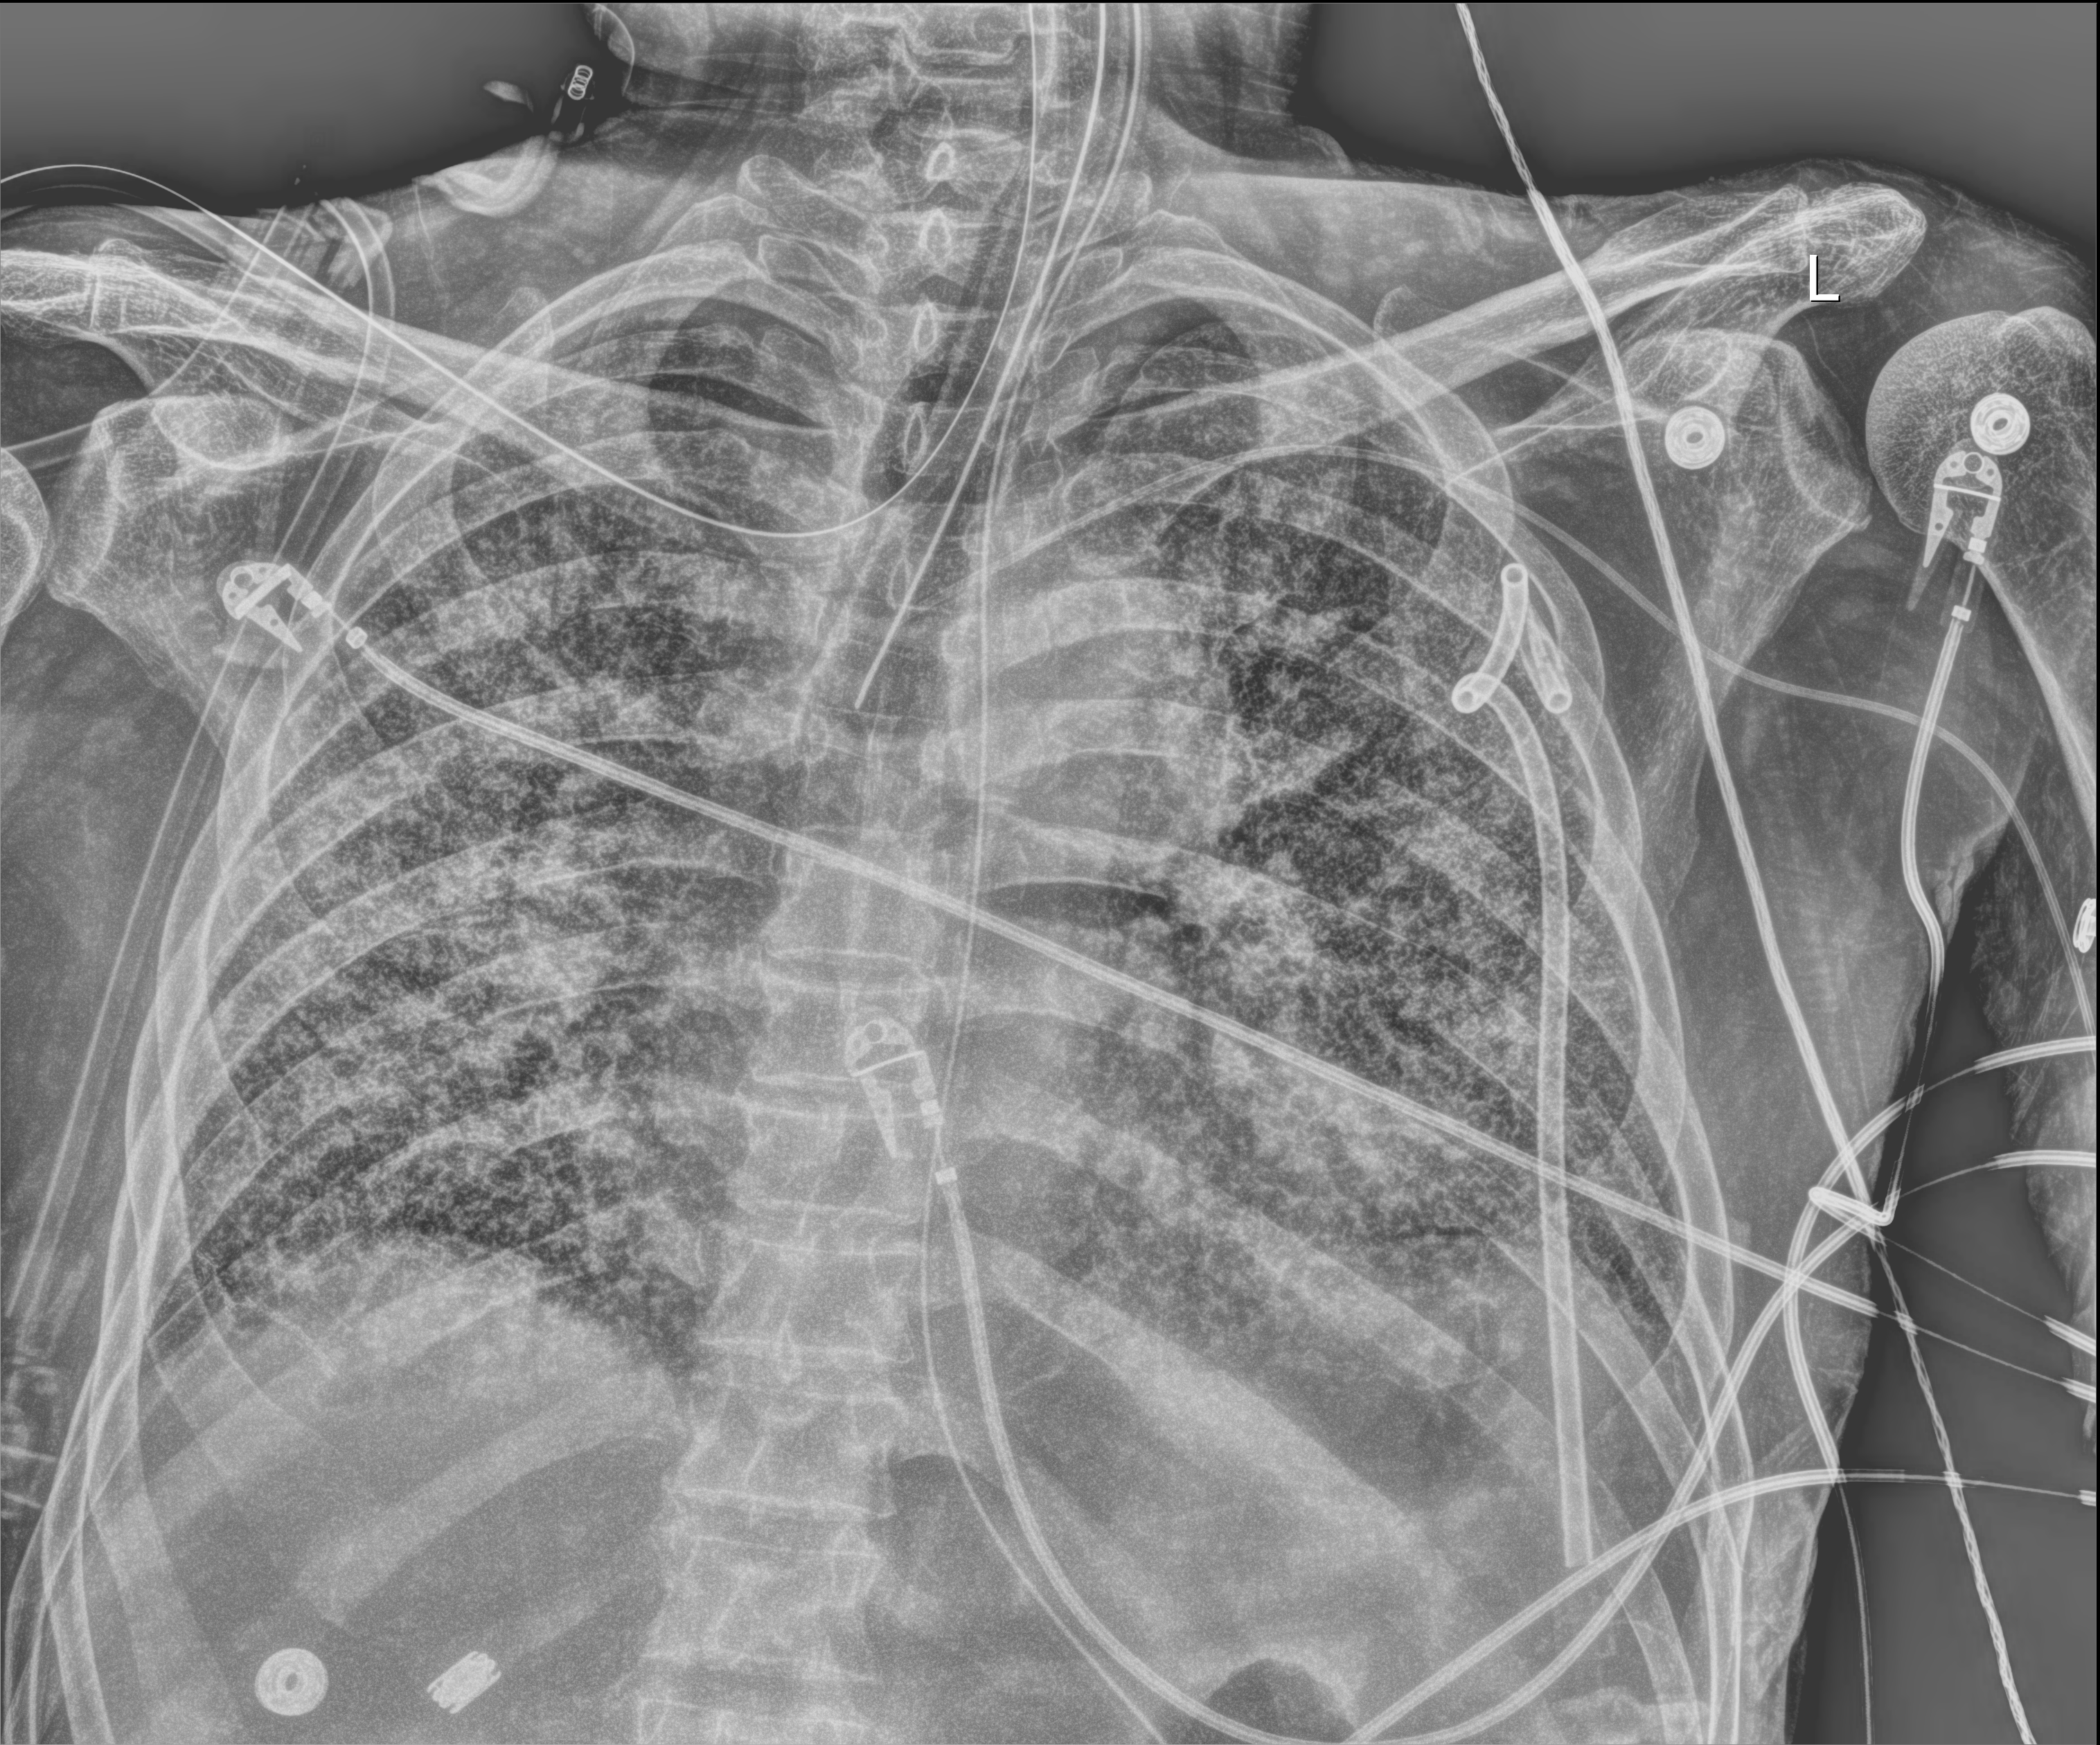
Chest X-ray; anteroposterior (AP) projection. Male patient hospitalised with COVID-19, age 60–74 years.
Hospital-stay facts (about this admission, not read from this image; timing relative to this image not recorded): admitted to intensive care during this hospital stay: yes.